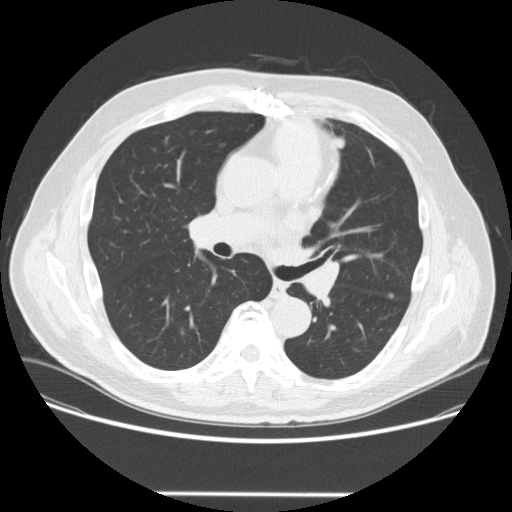
Chest CT (low-dose screening protocol), one axial image, third annual screen, lung window (W 1500 / L -600 HU), 2.5 mm slice thickness, standard (soft-tissue) reconstruction kernel (STANDARD), slice 102 of 253 in the series, 512 × 512 image matrix, field of view 400 × 400 mm. Male, age 66 years at enrolment. Former smoker at enrolment.
Expert-annotated lung lesion, bounding box [x1, y1, x2, y2] px = [298, 210, 351, 257]. The screening reader recorded 2 non-calcified nodules or masses ≥4 mm on this exam; which of them this box marks is not recorded. Official screen result: positive, other. Lung cancer was diagnosed 85 days after this screen: squamous cell carcinoma, NOS, left upper lobe, poorly differentiated (G3), stage IA (AJCC 6th edition), 27 mm at pathology.